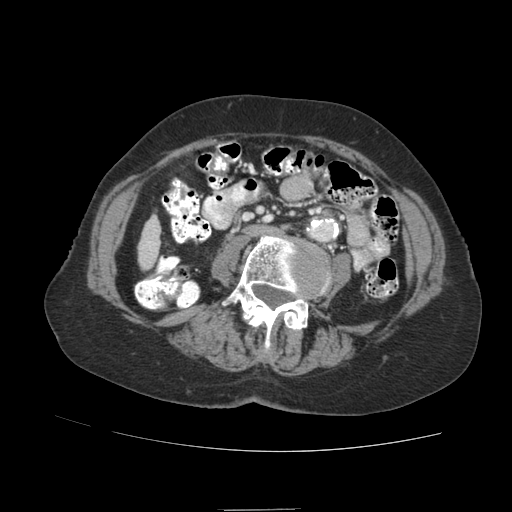
Contrast-enhanced abdominal CT (liver protocol), one axial slice. Slice 9 of 89 in the series (ordered by position). Soft-tissue window (W 400 / L 40 HU). 2.5 mm slice thickness. 512 × 512 image matrix, field of view 360 × 360 mm. From the clinical record (not read from this slice): diagnosis: hepatocellular carcinoma (patient treated with transarterial chemoembolisation; whether this scan precedes or follows treatment is not stated here); TNM stage (as recorded): Stage-II; Child-Pugh class: A; tumour differentiation: moderately differentiated; tumour nodularity: multinodular.
Outlined on this slice (semi-automatic segmentation, software-assisted and operator-edited):
- liver parenchyma outside the tumour (the mass and vessels are separate outlines, so this box may not span the whole liver): bounding box (x1, y1, x2, y2) in pixels: (138, 215, 160, 269)
- liver vessels: (148, 241, 150, 243)